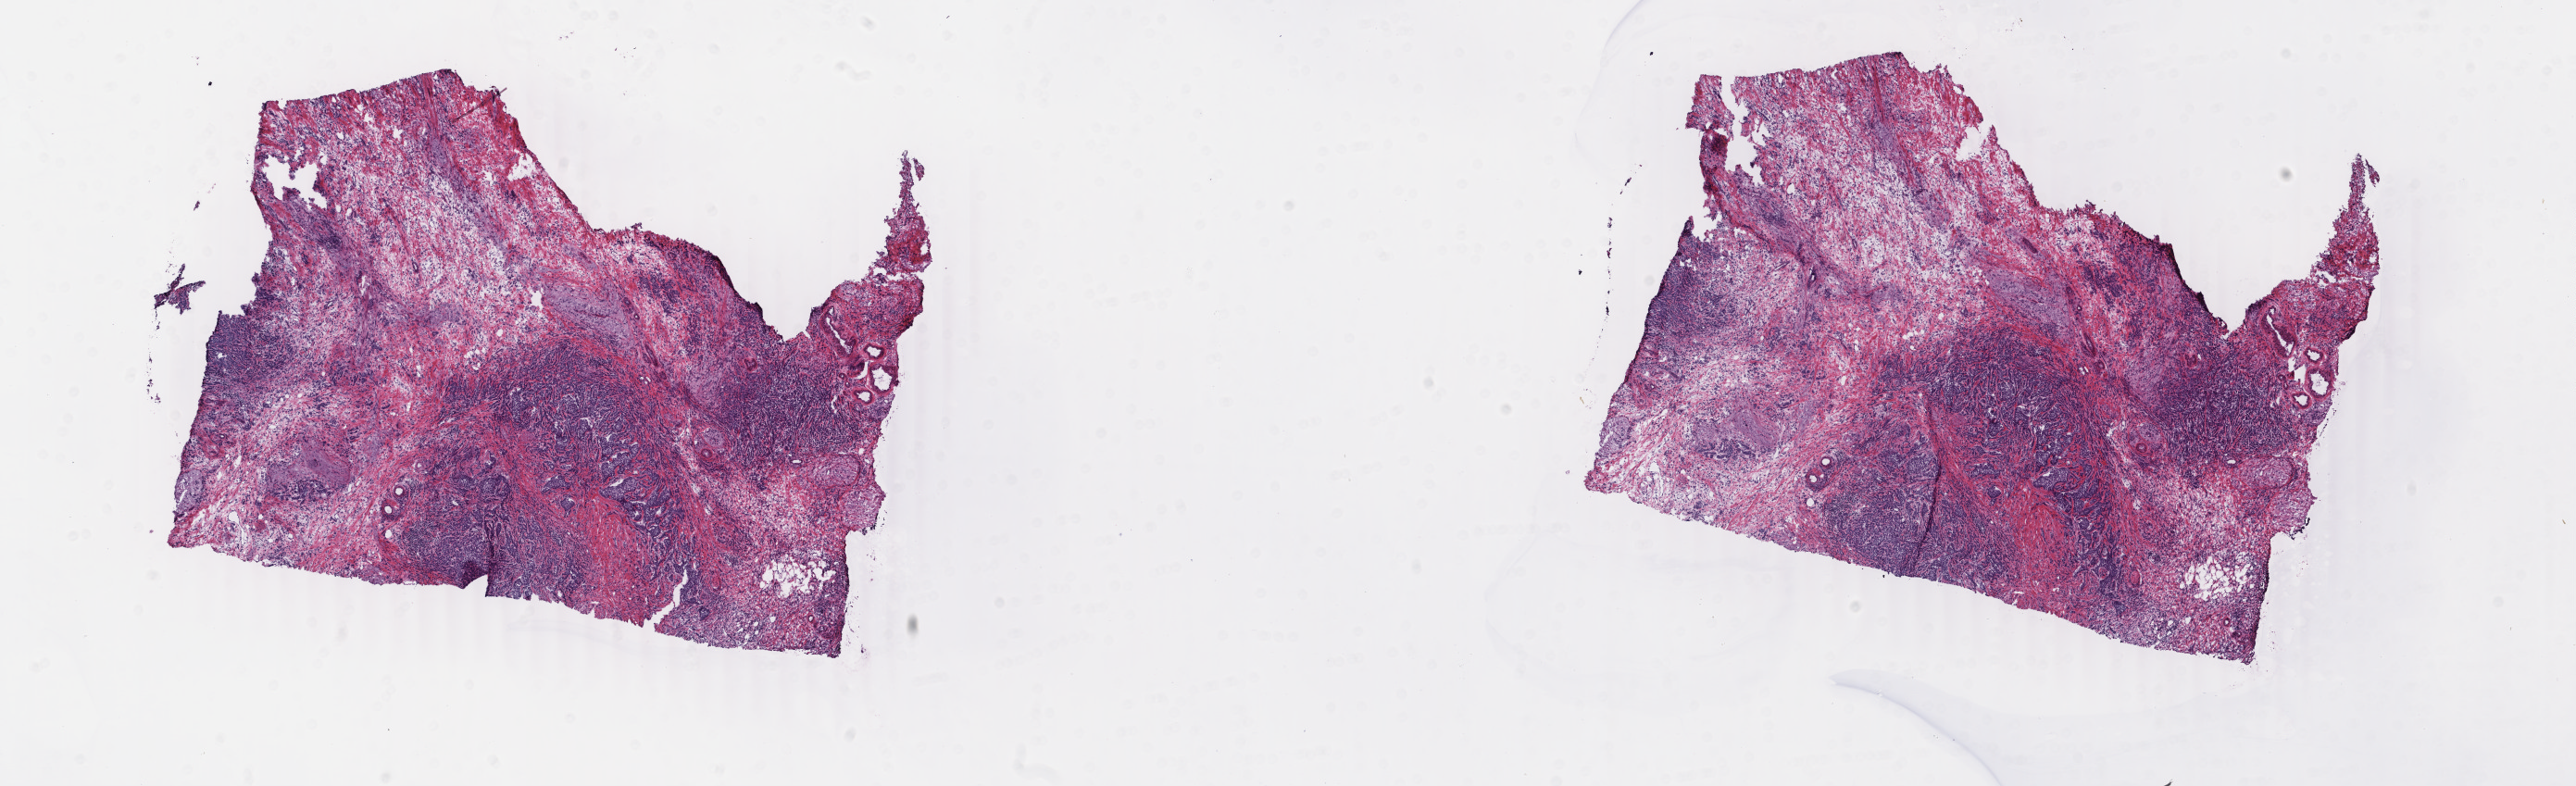
Hematoxylin and eosin (H&E) stained whole-slide image — shown as a low-resolution overview of the whole scanned area (about 22.1 x 6.8 mm, acquisition: 40x scan). Frozen section from the bottom of the tissue portion. Breast, primary tumour sample. Patient: female, age at initial diagnosis 62 years. Slide review estimates, as recorded: tumour cells 45%, tumour nuclei 70%, normal cells 0%, stromal cells 54%, necrosis 1%. Inflammatory infiltration, as recorded: lymphocyte infiltration 3%, monocyte infiltration 0%, neutrophil infiltration 1%.
• TNM: T2 N1a M0
• AJCC pathologic stage: IIB
• histologic diagnosis: Infiltrating duct carcinoma, NOS